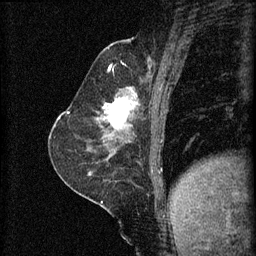
Breast MRI (dynamic contrast-enhanced), one sagittal slice. Position 26 of 60 along the scan axis. 3 images stored at this slice position (order not interpretable as contrast timing). 1.5 T. TE 4.2 ms, TR 8.2 ms. 2 mm slice thickness. 256 × 256 image matrix. Patient: female, 59 years.
Outlined on this slice (semi-automatically segmented with operator editing):
- analysis volume of interest (the breast-tissue region the enhancement analysis was run in; not a lesion): bounding box (x1, y1, x2, y2) in pixels: (96, 92, 137, 135)
- tumour enhancement mask (voxels above the 70 % enhancement threshold inside the analysis volume of interest): (98, 94, 137, 129)